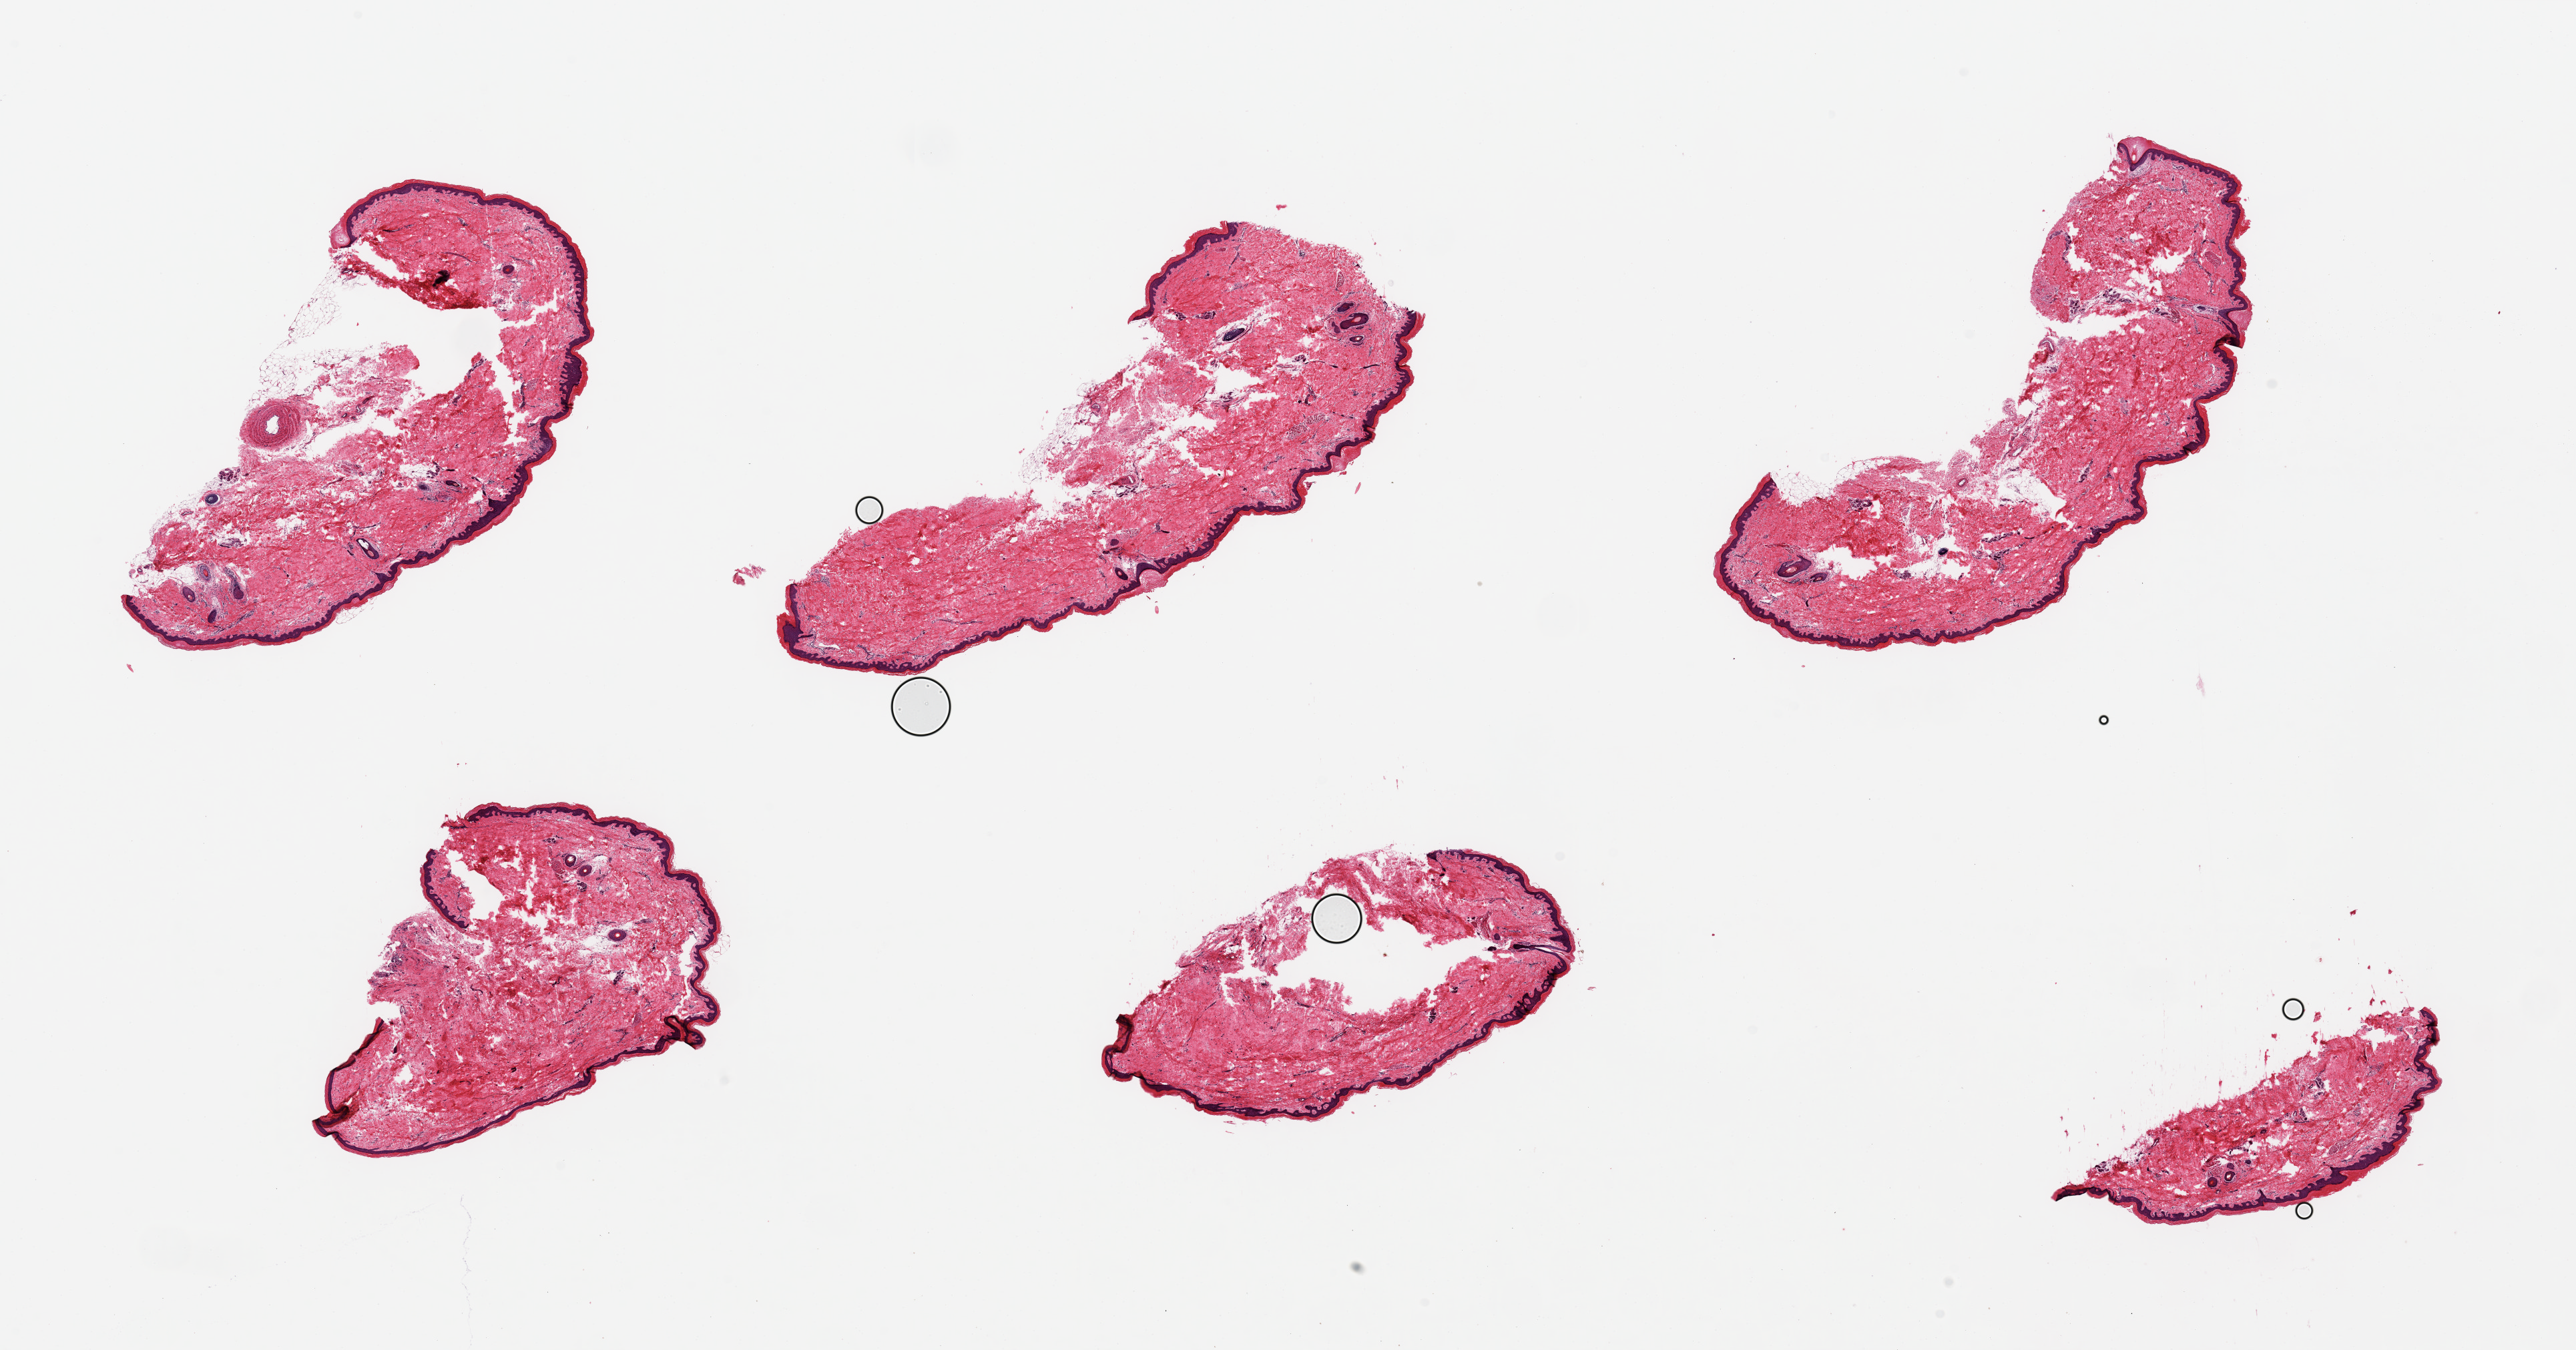
Whole-slide image, H&E stain, whole scanned area (about 30.5 x 16.0 mm) shown as a low-resolution overview; PAXgene-fixed, paraffin-embedded tissue; section of skin of lower leg (target tissue); donor tissue sample. Donor sex: female.
Reviewer comment on this tissue sample: 6 pieces, up to 8x3mm; most subcutaneous adipose removed; keratin layer looks thicker than usual.